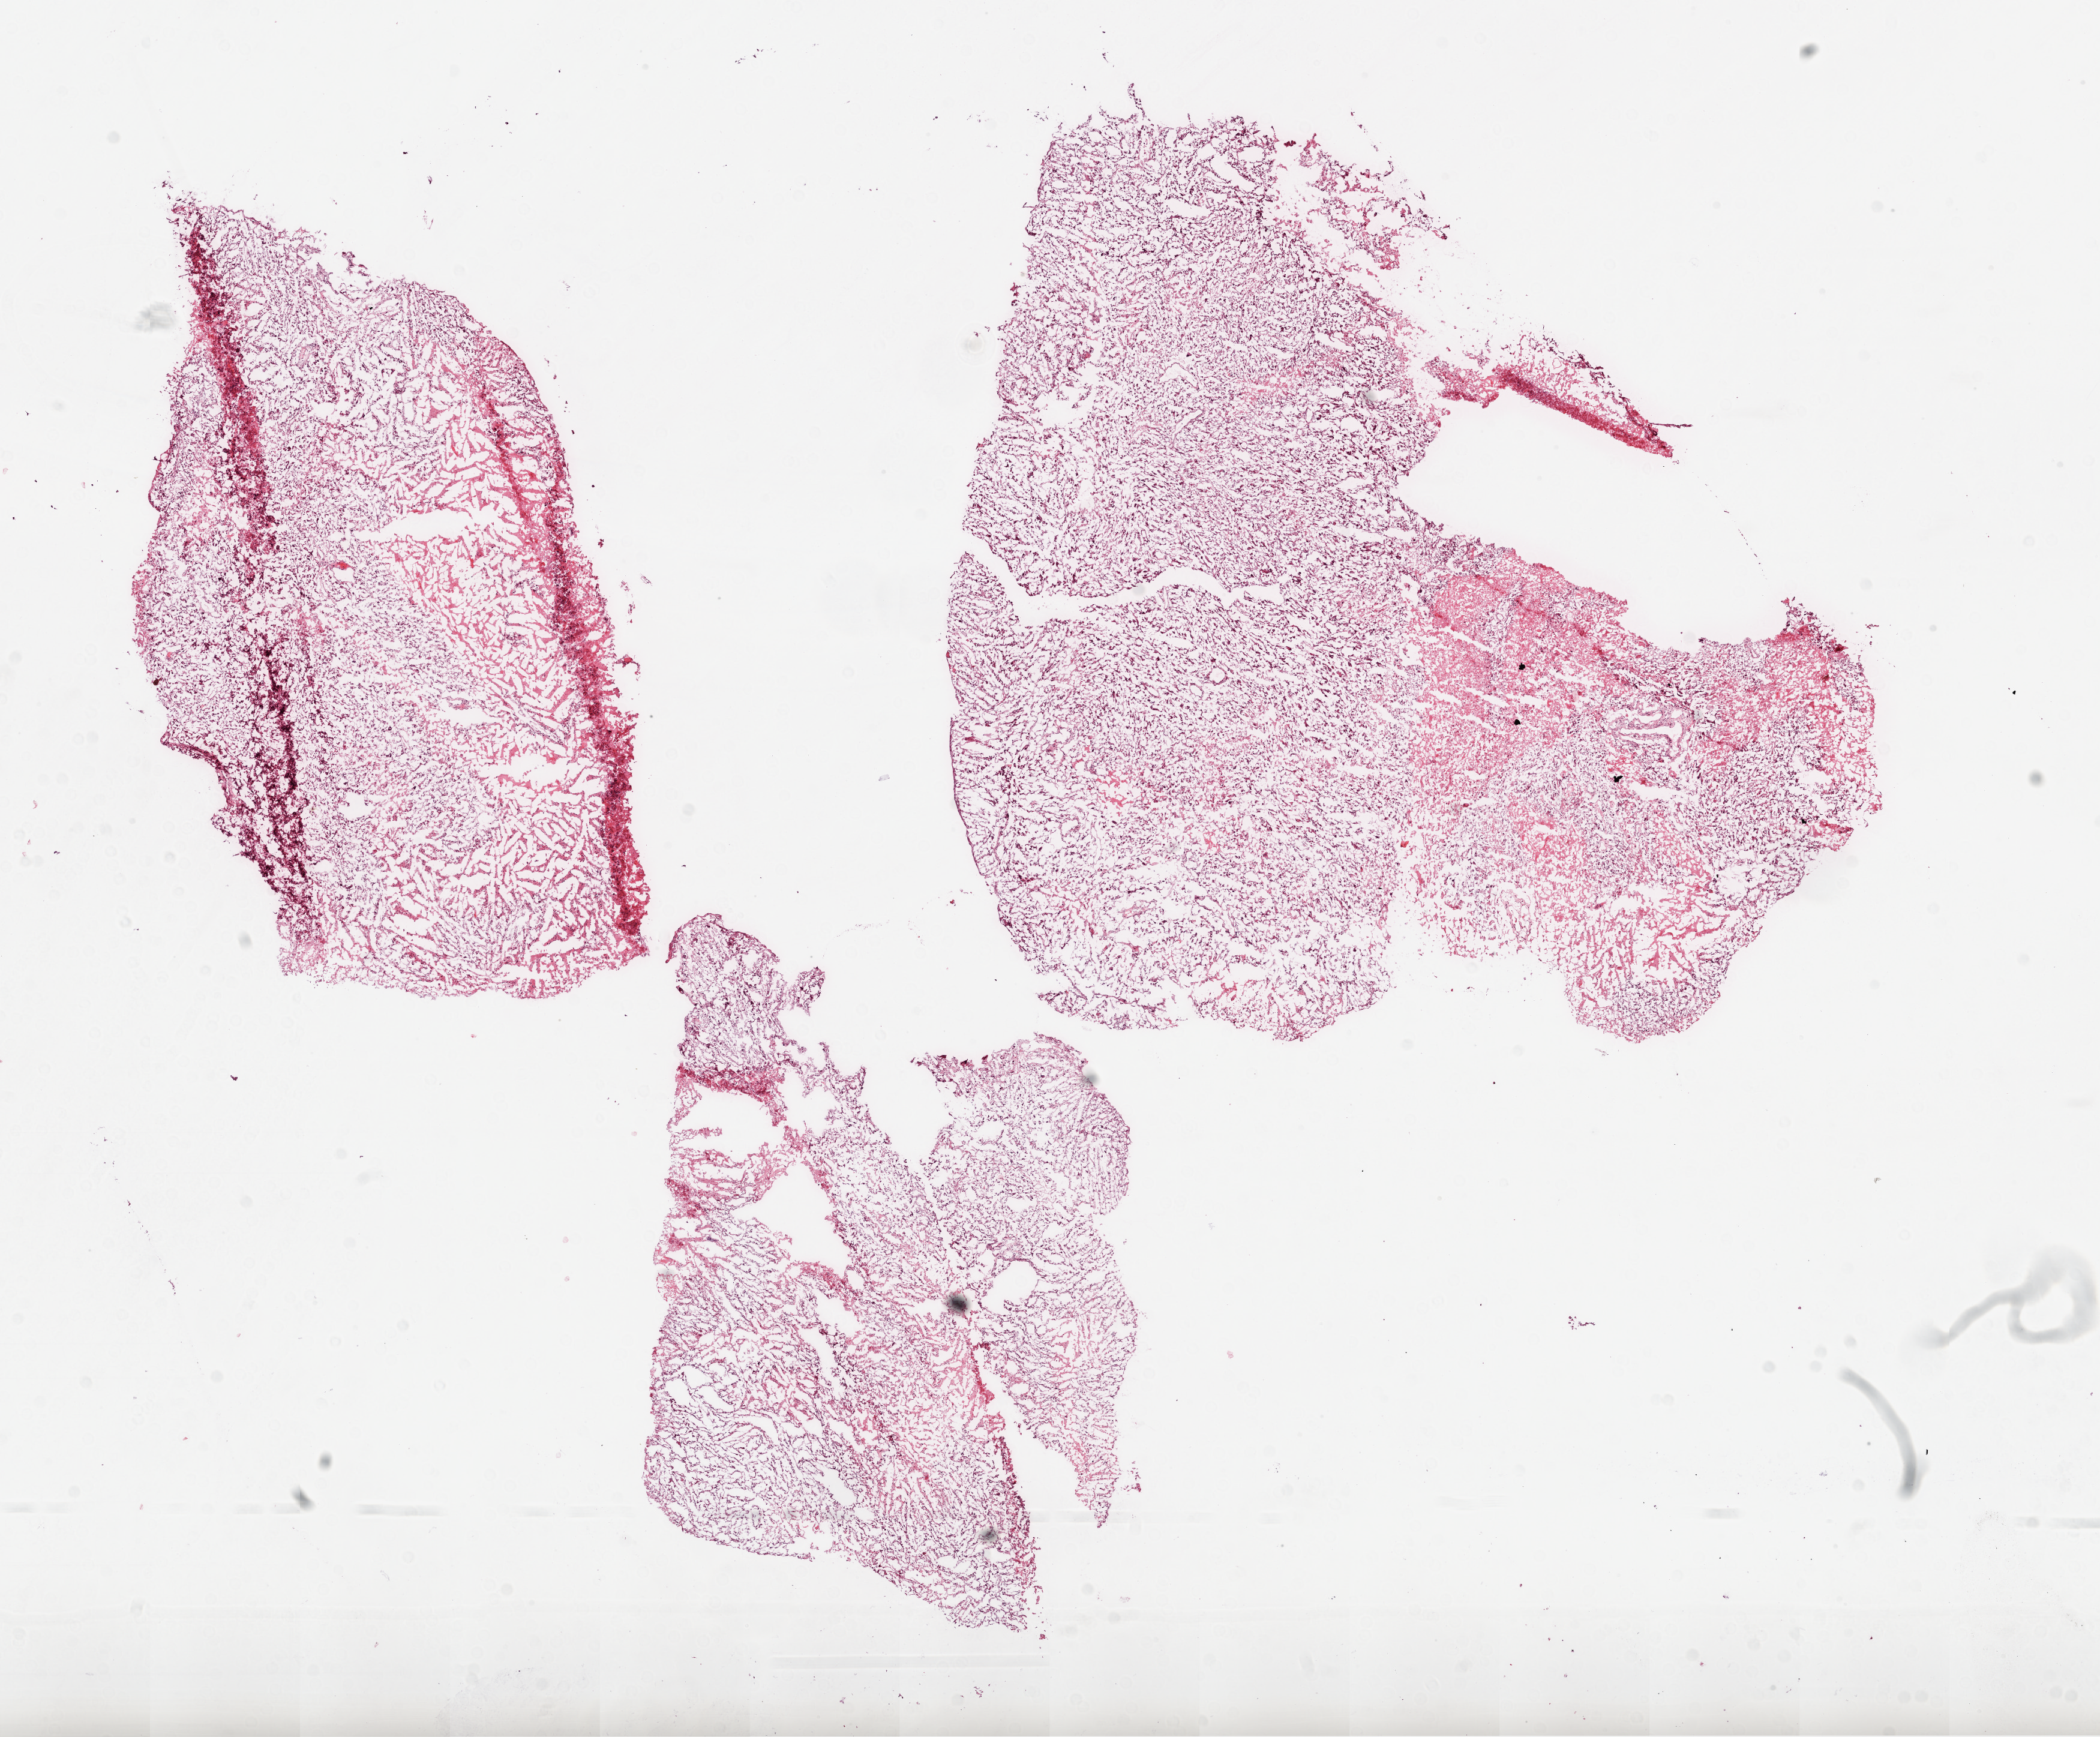
Whole-slide histology image, H&E-stained, whole scanned area (about 14.0 x 11.6 mm, acquisition: 20x scan) shown as a low-resolution overview. Frozen section. Brain, primary tumour sample. Patient: female, age at initial diagnosis 78 years.
Diagnosis: Glioblastoma.